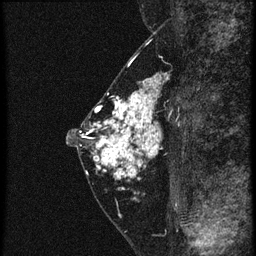
Breast MRI (dynamic contrast-enhanced), one sagittal slice; position 30 of 60 along the scan axis; 4 images stored at this slice position (order not interpretable as contrast timing); 1.5 T; TE 4.2 ms, TR 20.4 ms; 256 × 256 image matrix, field of view 180 × 180 mm. Patient: female, 46 years. From the clinical record (not read from this slice): setting: breast cancer imaged before/during neoadjuvant chemotherapy; receptor status: triple-negative.
Outlined on this slice (semi-automatic segmentation, software-assisted and operator-edited):
- analysis volume of interest (the breast-tissue region the enhancement analysis was run in; not a lesion): box from (x=88, y=82) to (x=173, y=185) px
- tumour enhancement mask (voxels above the 90 % enhancement threshold inside the analysis volume of interest): (x=90, y=82)–(x=161, y=179)